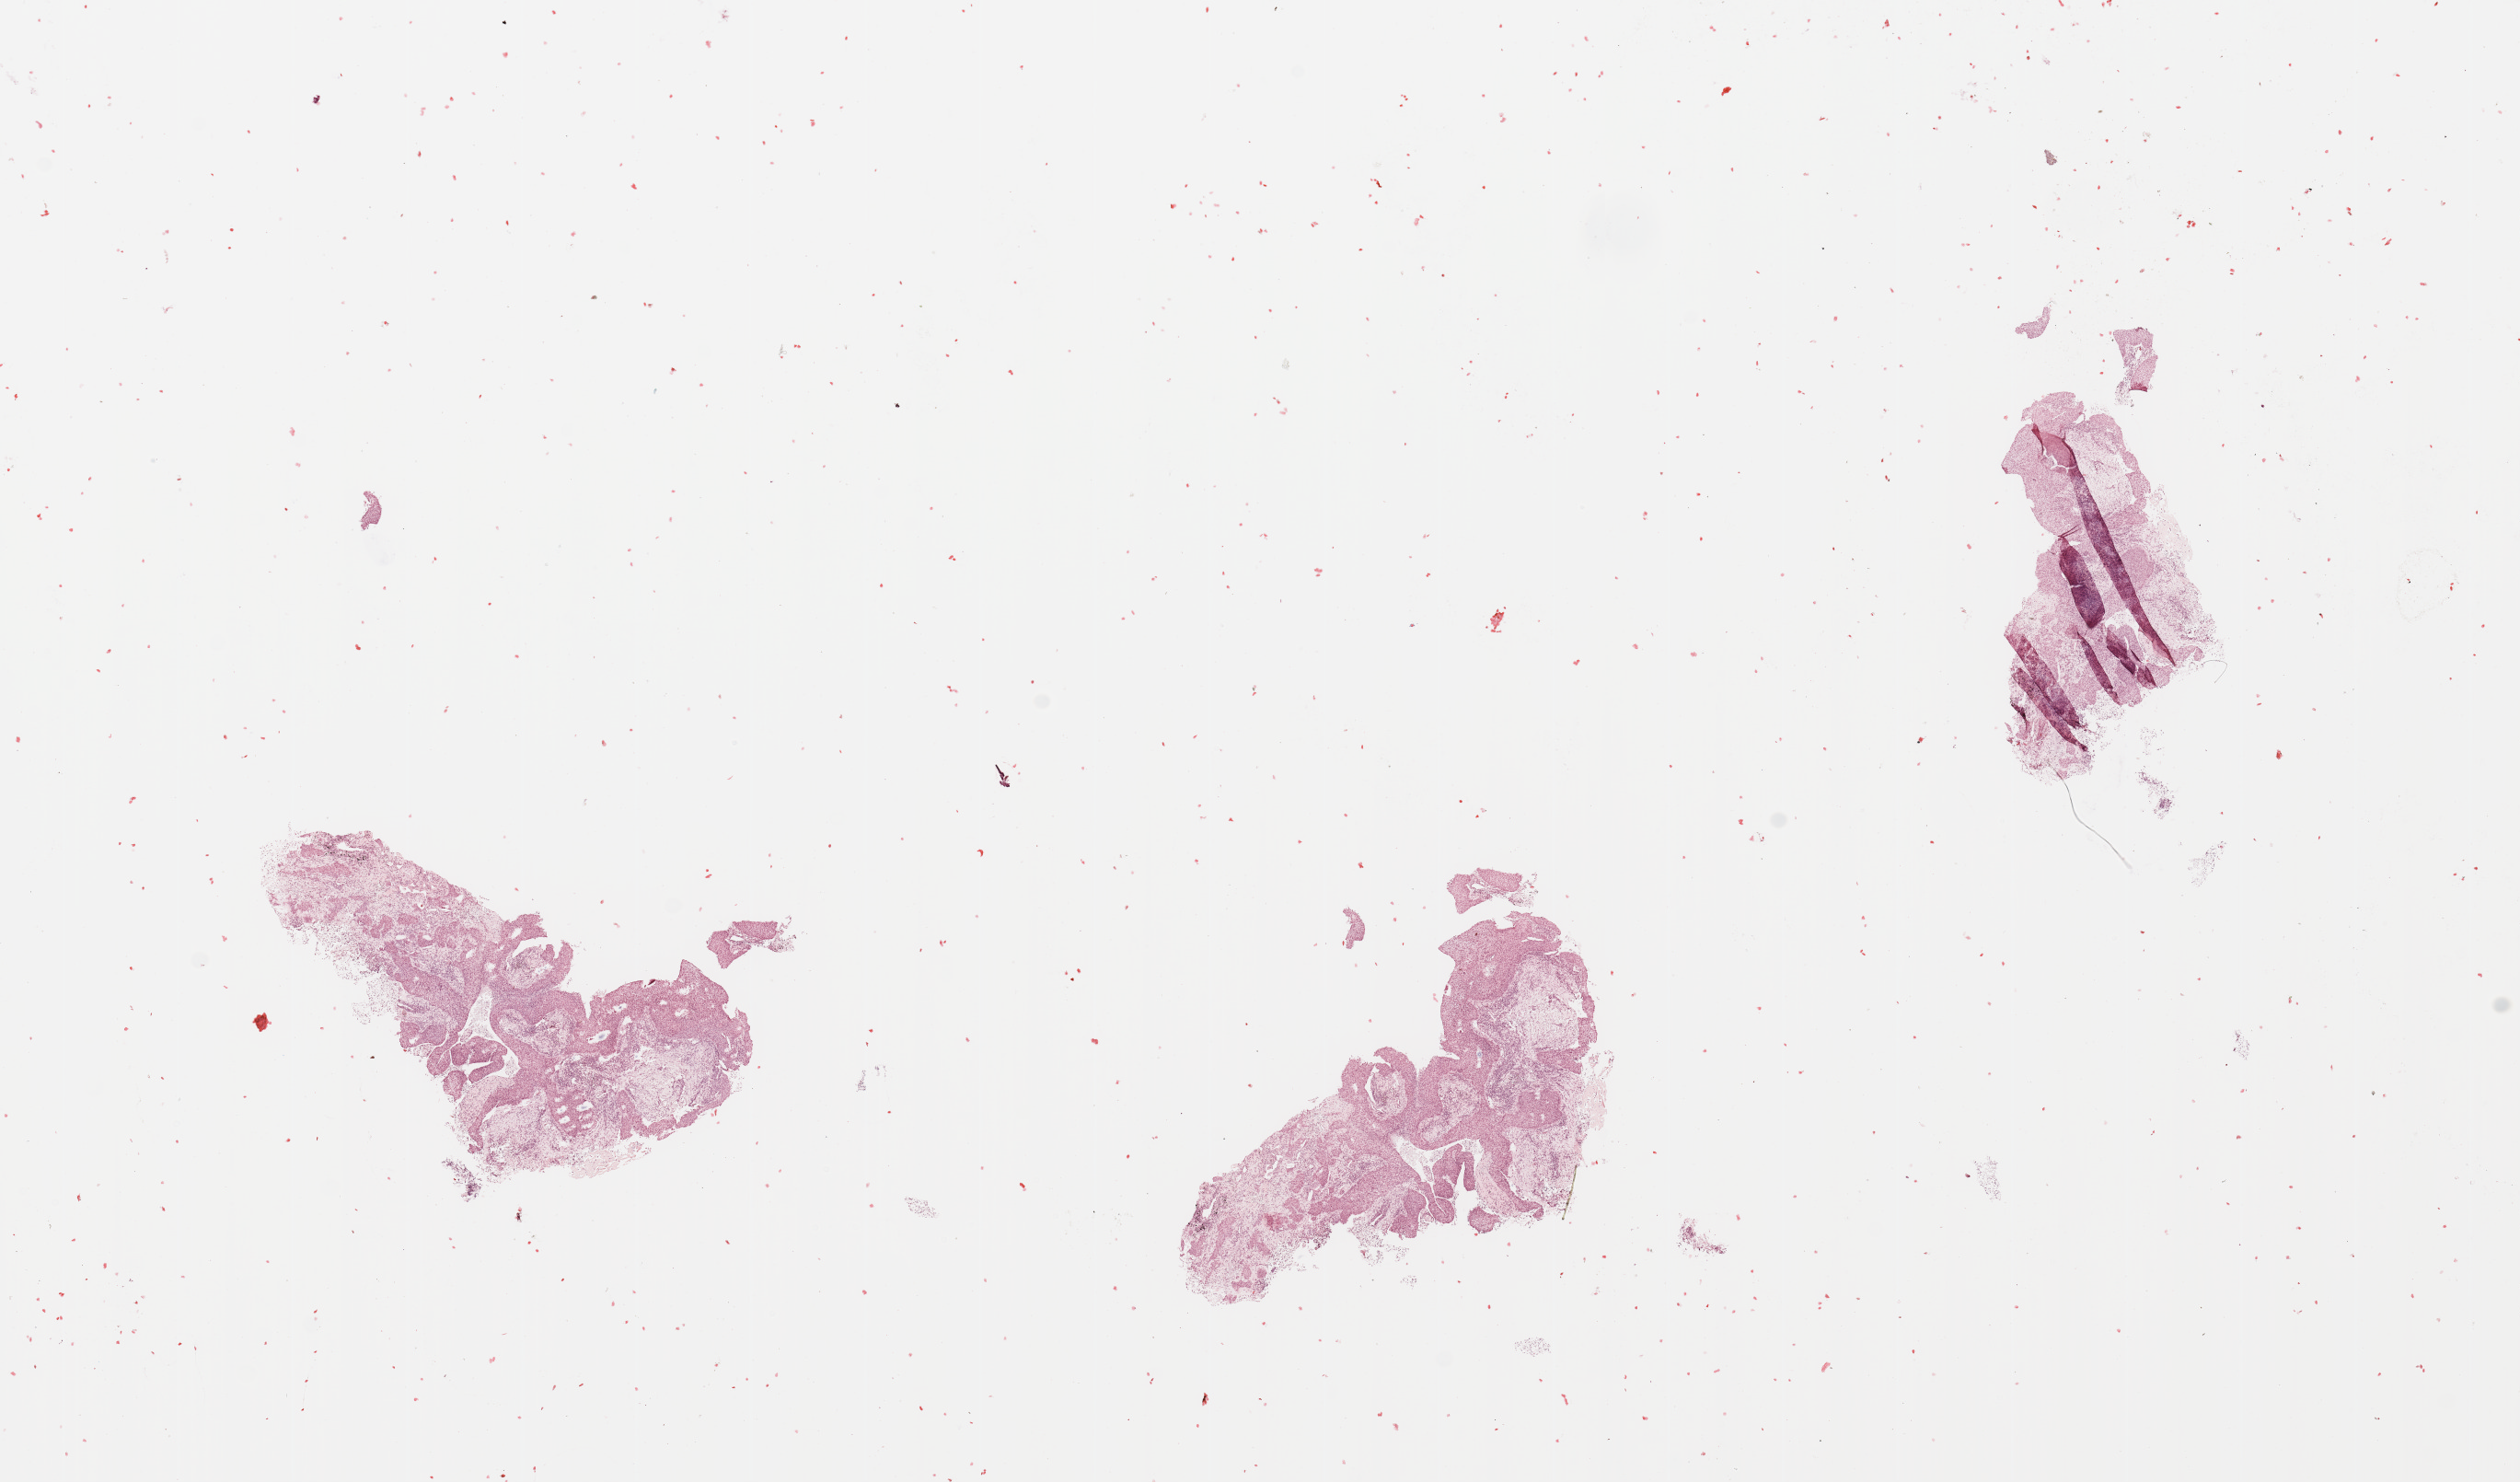
Digitized H&E-stained tissue section (whole slide), a low-resolution overview of the entire scanned area, about 21.7 x 12.7 mm (from a 20x scan), lung, tumour tissue. 69-year-old female patient. Histologic grade: G2 (moderately differentiated).
Primary tumour site (as recorded): left upper lobe. AJCC pathologic stage: IIB. Histologic diagnosis: Squamous cell carcinoma, NOS.